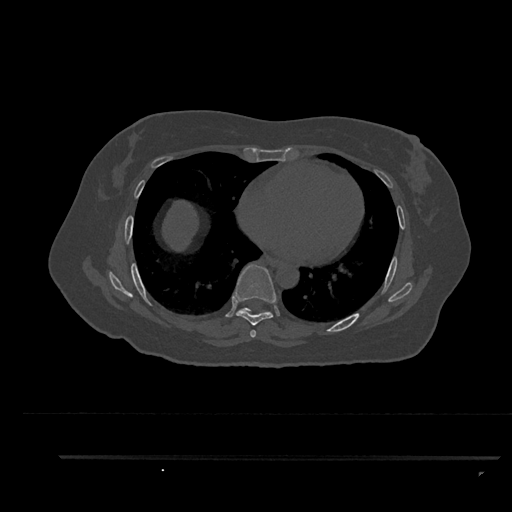
CT including the spine, one axial slice; reconstruction kernel Br40s/3; bone window (W 1800 / L 400 HU); 512 × 512 image matrix, field of view 408 × 408 mm. Patient: female, 44 years. Case-level facts recorded for this patient, not image findings: primary cancer: renal.
Structures marked on this image (semi-automatic segmentation, software-assisted and operator-edited):
- T6 vertebra: box from (x=251, y=330) to (x=256, y=338) px
- T7 vertebra: (x=233, y=264)–(x=276, y=338)
- T8 vertebra: (x=236, y=308)–(x=268, y=315)